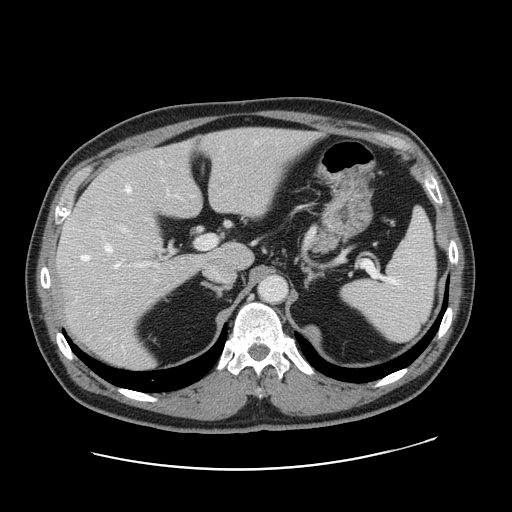
Contrast-enhanced abdominal CT, one axial slice. Position 105 of 178 along the scan axis. 120 kVp. Intravenous contrast given. Soft-tissue window (W 400 / L 40 HU). 2.5 mm slice thickness. 512 × 512 image matrix, field of view 403 × 403 mm. Male patient, age 63 years. From the clinical record (not read from this slice): diagnosis: colorectal cancer liver metastases, imaged before liver resection.
Annotated regions visible in this slice (expert manual segmentation):
- hepatic veins: bounding box <82,185,131,266> (left, top, right, bottom; pixels)
- liver: <58,128,312,370>
- planned liver remnant (the part of the liver to remain after resection): <125,128,311,268>
- portal vein (with intrahepatic branches): <120,227,217,266>
- liver metastasis: <72,208,93,227>